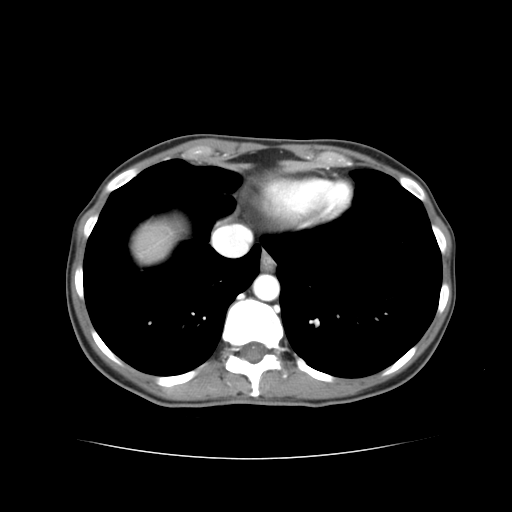
Contrast-enhanced abdominal CT, one axial slice. Slice 36 of 38 in the series (ordered by position). Reconstruction kernel STANDARD. 120 kVp. Intravenous contrast given. Soft-tissue window (W 400 / L 40 HU). 5 mm slice thickness. 512 × 512 image matrix, field of view 340 × 340 mm. Female patient, age 54 years. Case-level facts recorded for this patient, not image findings: diagnosis: colorectal cancer liver metastases, imaged before liver resection; multiple liver metastases: yes; largest metastasis: 1.1 cm; chemotherapy before resection: yes.
Annotated regions visible in this slice (outlined manually by an expert reader):
- liver: bounding box (x1, y1, x2, y2) in pixels: (139, 222, 170, 257)